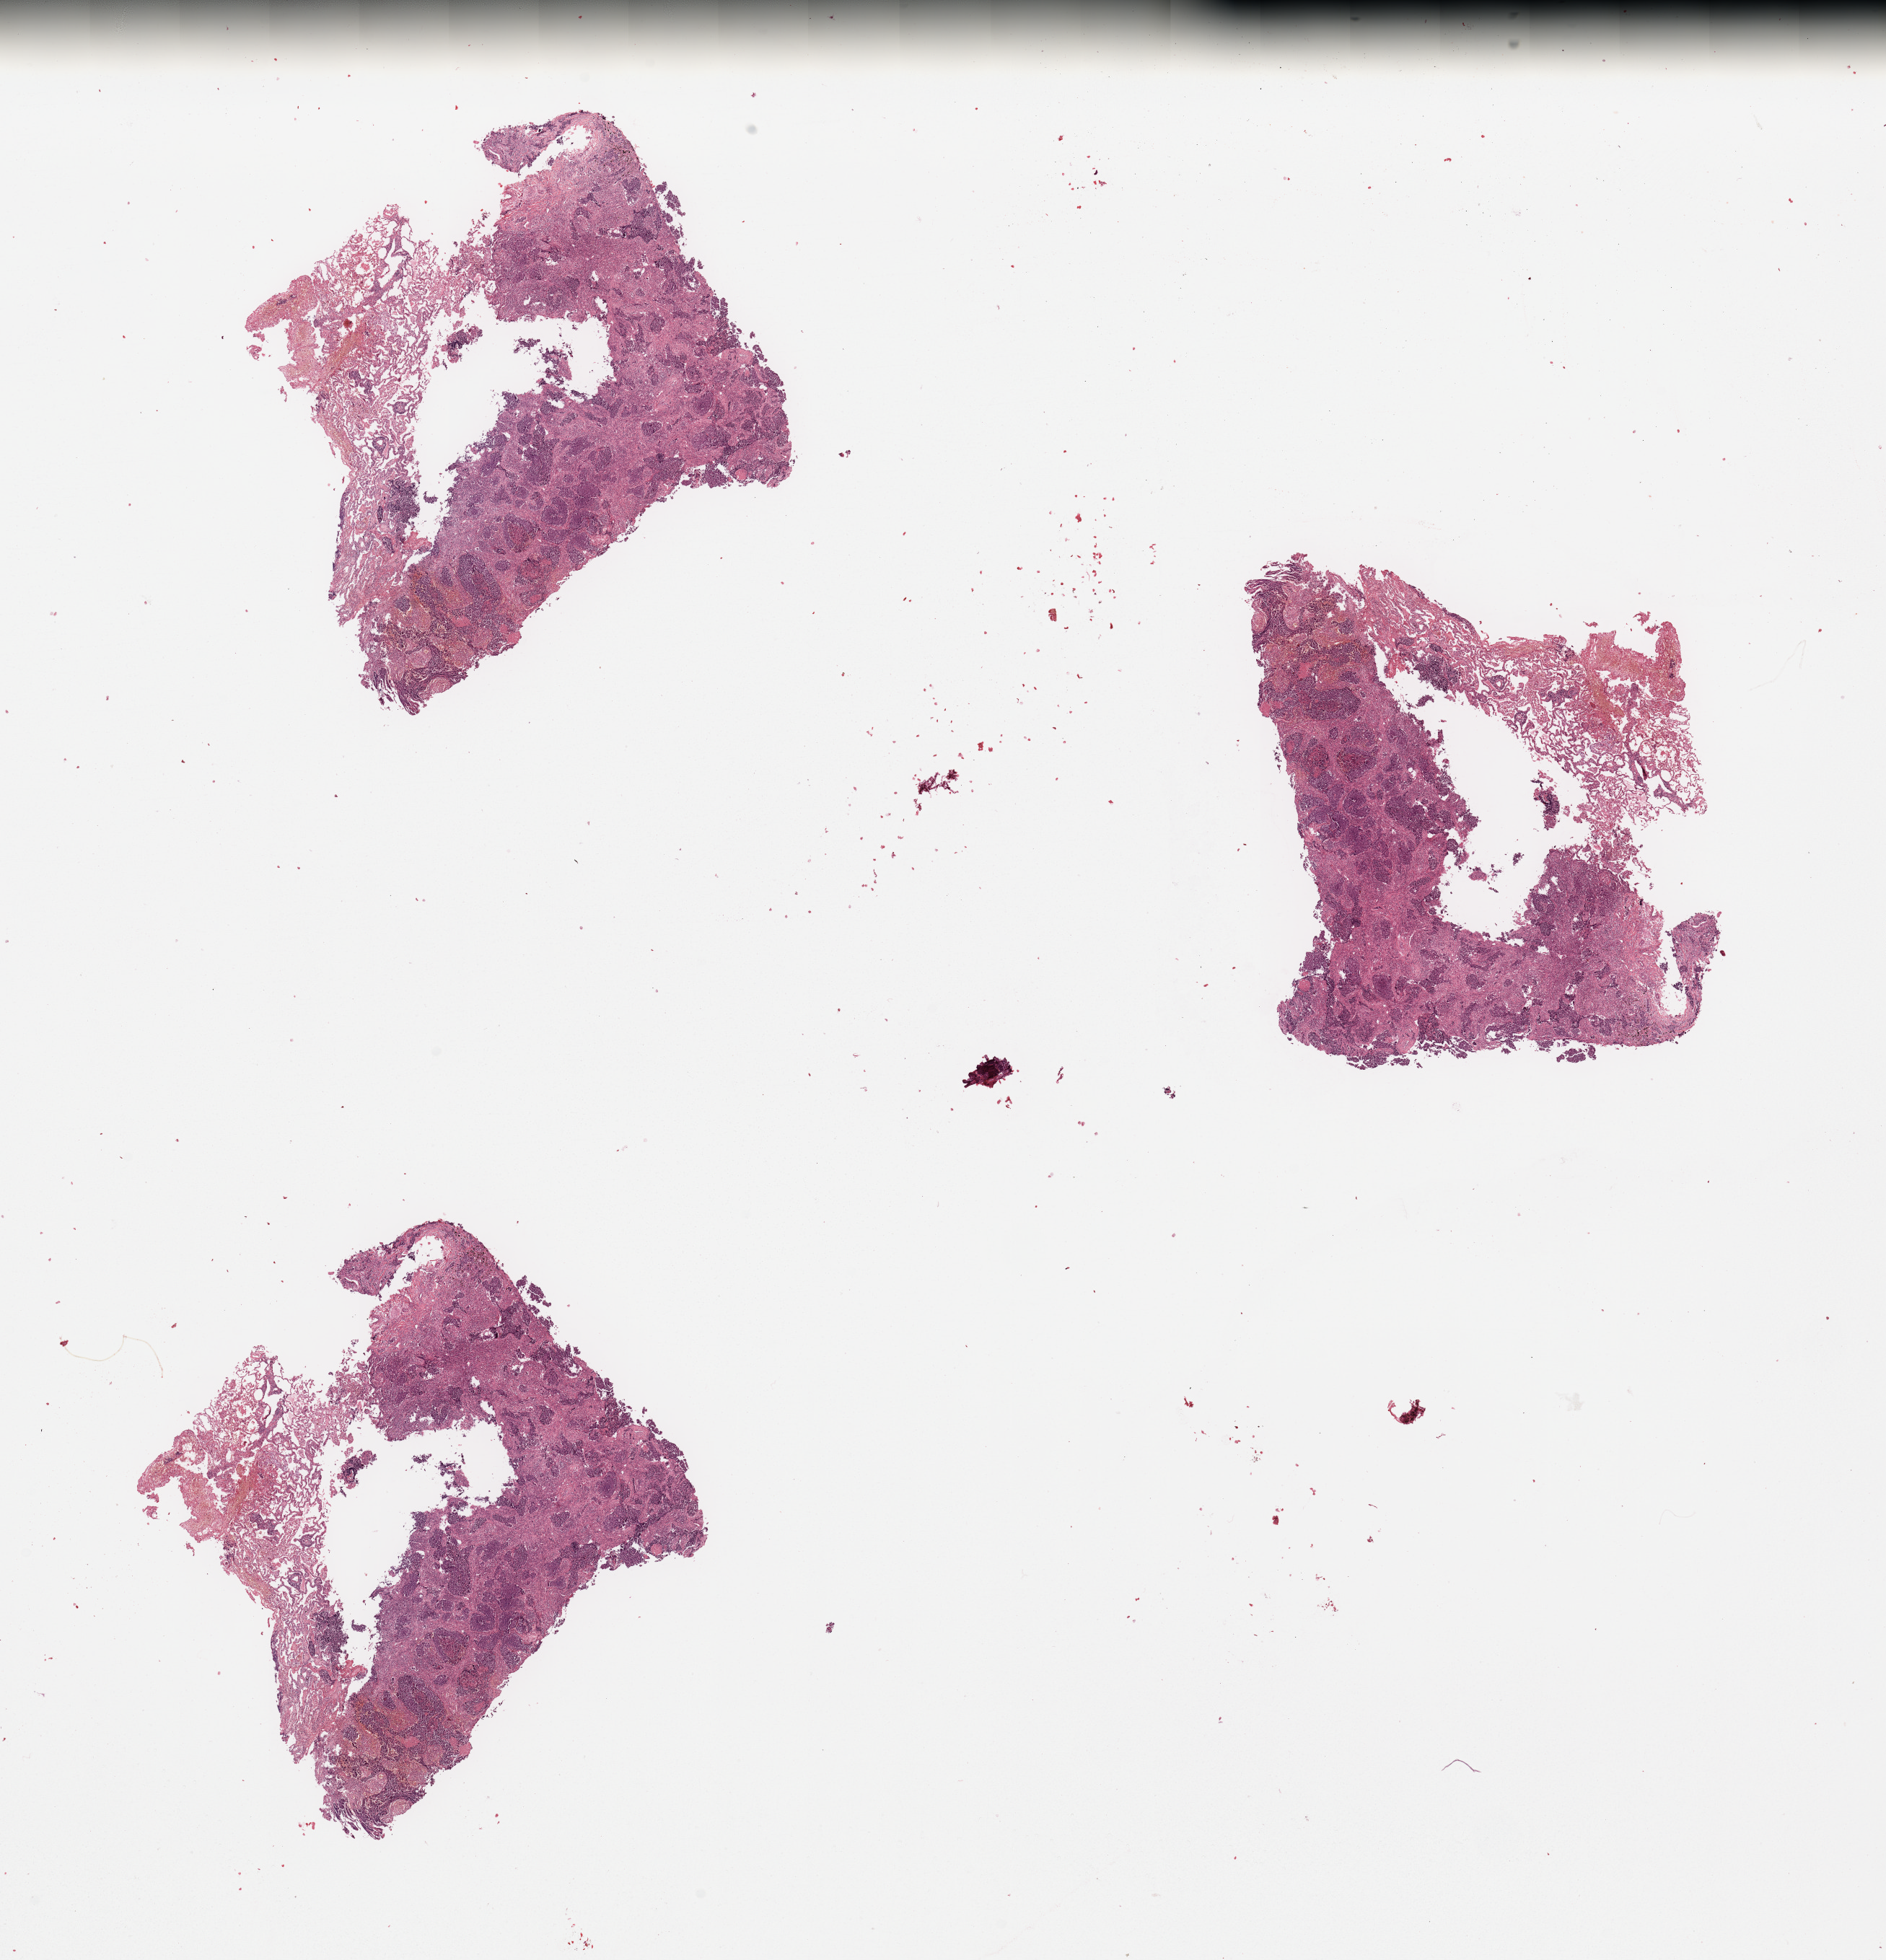
Whole-slide histology image, Hematoxylin and eosin (H&E) stained, low-resolution overview of the scanned area, about 20.7 x 21.5 mm, lung, tumour tissue. Male, 54 y/o. Histologic grade: G2 (moderately differentiated).
Histologic diagnosis: Adenocarcinoma, NOS. Primary tumour site (as recorded): left upper lobe. AJCC pathologic stage: IA.